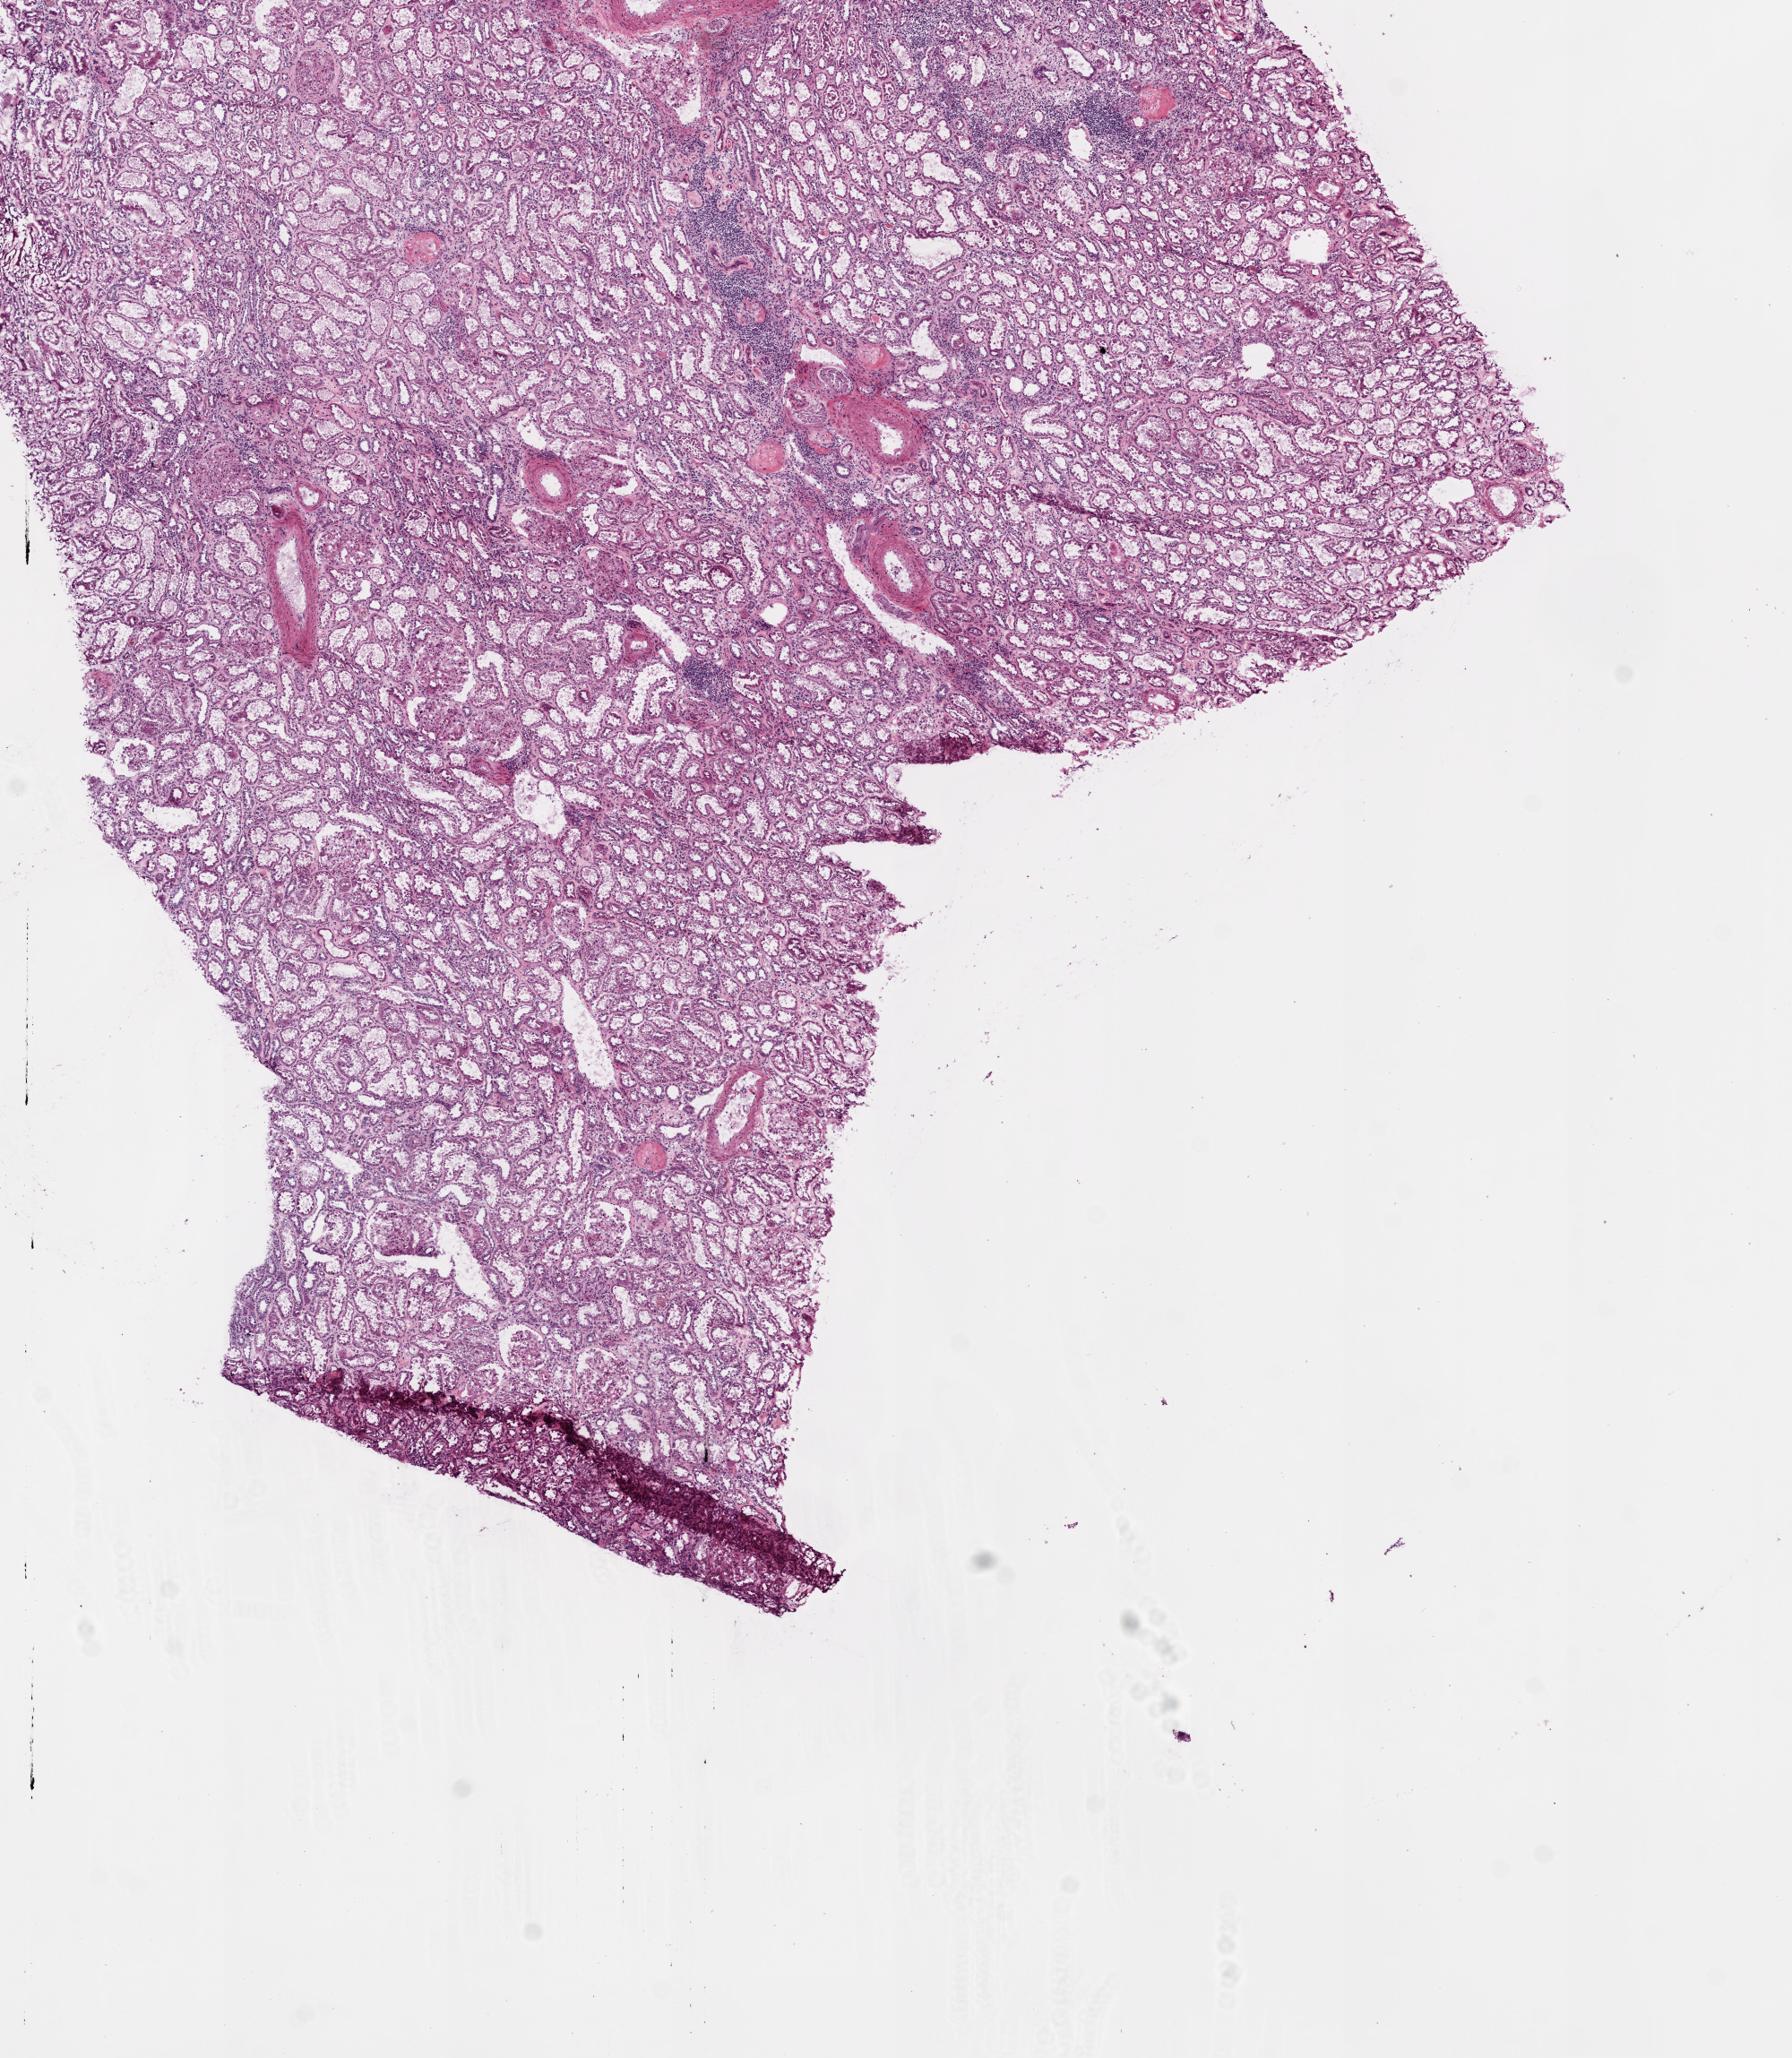
Whole-slide histology image, Hematoxylin and eosin (H&E) stained — a low-resolution overview of the entire scanned area, about 8.0 x 9.2 mm (slide scanned at 20x); frozen section from the bottom of the tissue portion; solid tissue normal (non-tumour tissue) sample from the kidney. Patient: male, age at initial diagnosis 58 years.
This section: solid tissue normal sample (biorepository sample class). Patient diagnosis: Clear cell adenocarcinoma, NOS.